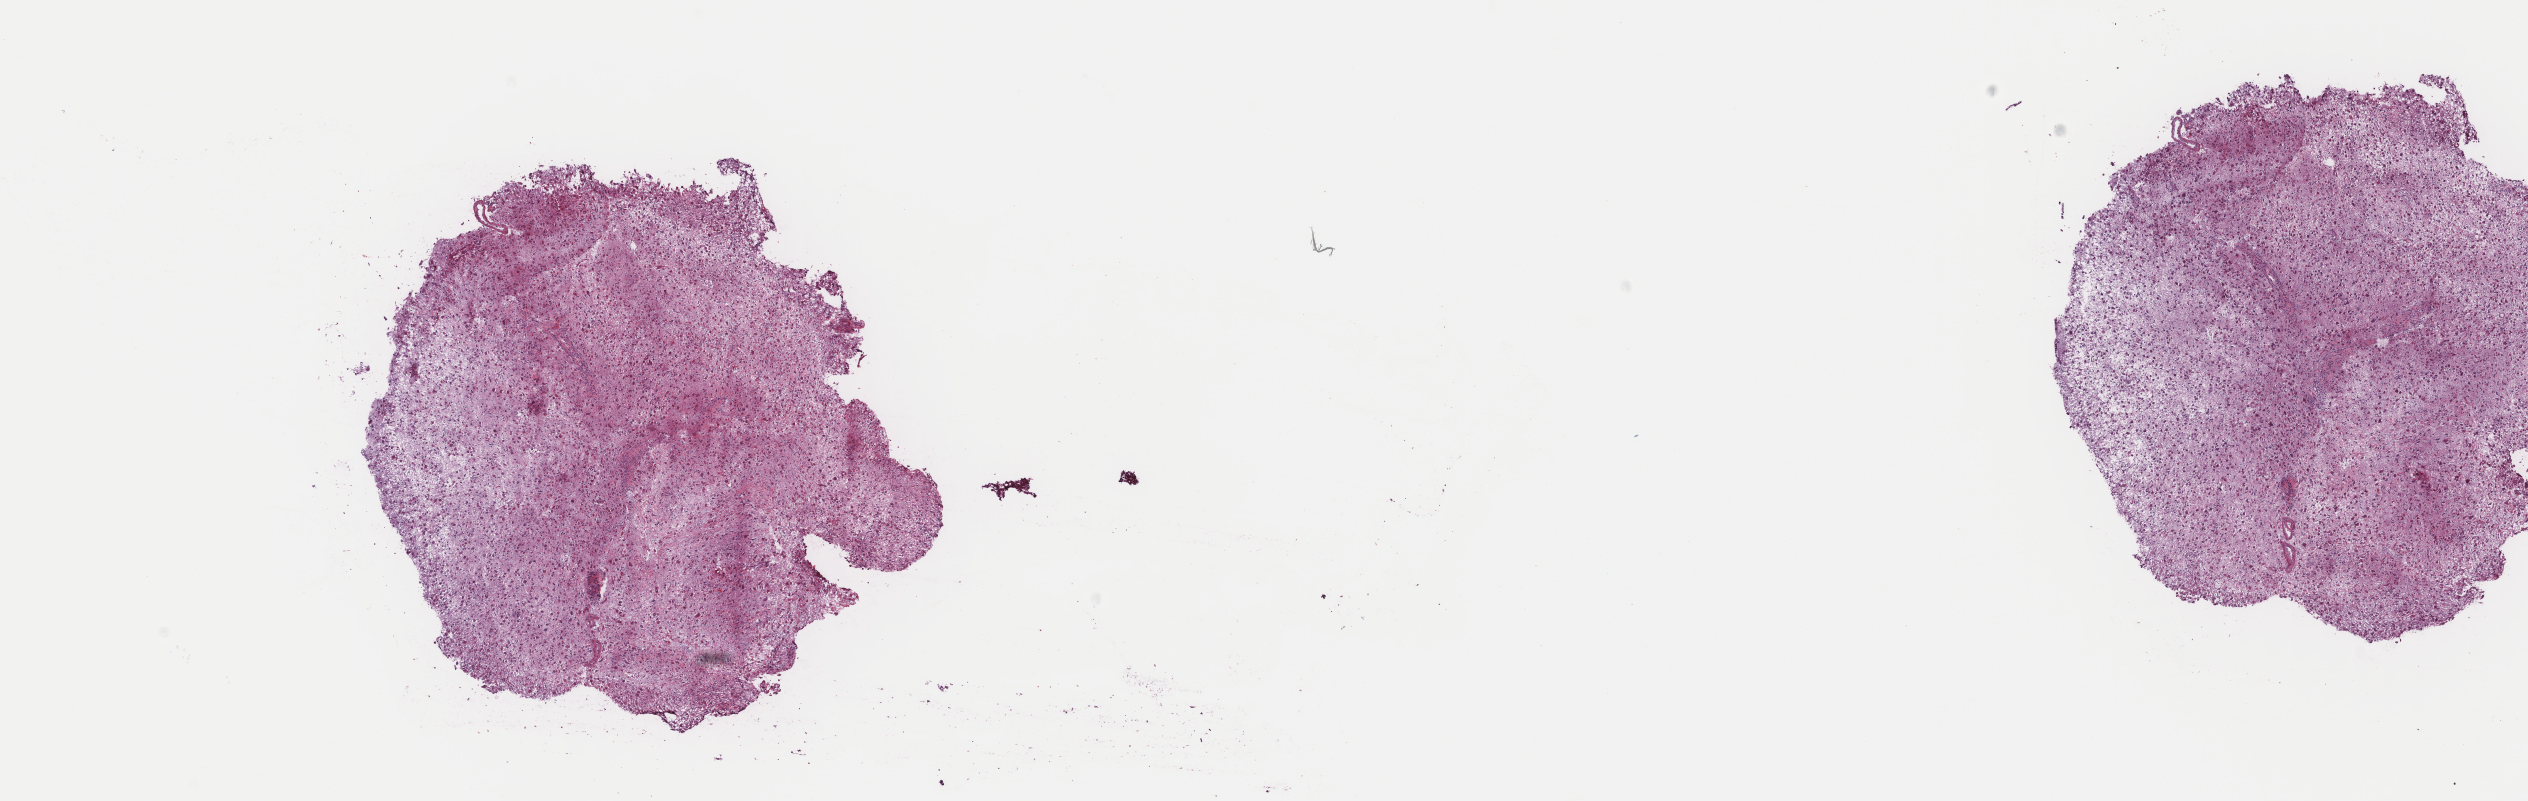
H&E whole-slide image, low-resolution overview of the scanned area, about 20.1 x 6.4 mm, frozen section from the top of the tissue portion, brain, primary tumour sample. Male, age 27 years at initial diagnosis. Histologic grade: G2 (moderately differentiated). Slide review estimates, as recorded: tumour cells 50%, tumour nuclei 90%, normal cells 10%, stromal cells 40%, necrosis 0%. Infiltration values recorded for this section: lymphocyte infiltration 0%, monocyte infiltration 0%, neutrophil infiltration 0%.
* laterality: left
* histologic diagnosis: Astrocytoma, NOS (cerebrum)